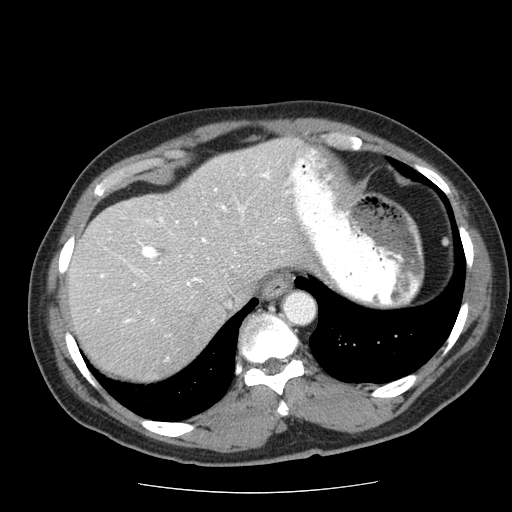
Contrast-enhanced abdominal CT (liver protocol), one axial slice; slice 50 of 85 in the series (ordered by position); reconstruction kernel STANDARD; 120 kVp; soft-tissue window (W 400 / L 40 HU); 2.5 mm slice thickness; 512 × 512 image matrix, field of view 360 × 360 mm. Case-level facts recorded for this patient, not image findings: diagnosis: hepatocellular carcinoma (patient treated with transarterial chemoembolisation; whether this scan precedes or follows treatment is not stated here); TNM stage (as recorded): Stage-IIIA; Child-Pugh class: A; tumour nodularity: multinodular; tumour size: 8 cm.
Structures marked on this image (semi-automatically segmented with operator editing):
- liver parenchyma outside the tumour (the mass and vessels are separate outlines, so this box may not span the whole liver): bounding box <68,138,360,380> (left, top, right, bottom; pixels)
- liver vessels: <98,150,360,323>